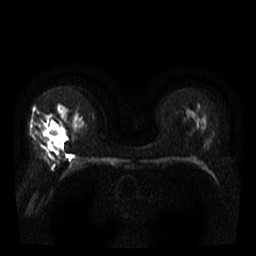
Breast MRI, one axial slice; slice 22 of 40 in the series (ordered by position); diffusion-weighted series; image 2 of 4 stored at this slice position (different b-values; order by instance number); 3 T; 5 mm slice thickness; 256 × 256 image matrix, field of view 300 × 300 mm. Female patient.
Structures marked on this image (expert manual segmentation):
- tumour on diffusion-weighted imaging: bounding box <37,125,64,147> (left, top, right, bottom; pixels)